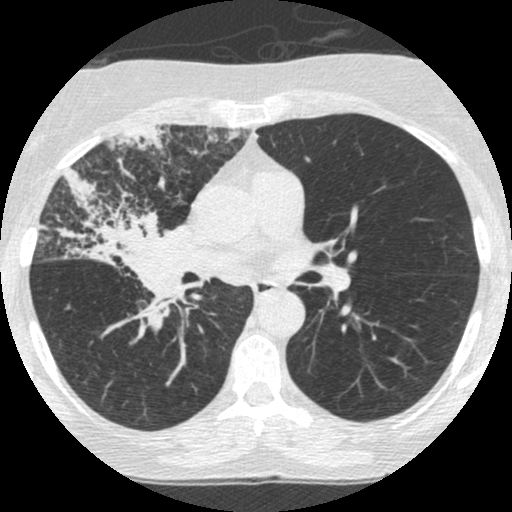
Low-dose screening chest CT, one axial slice; slice 145 of 253 in the series (ordered by position); lung window (W 1500 / L -600 HU); 1.25 mm slice thickness; 512 × 512 image matrix, field of view 294 × 294 mm.
Outlined on this slice (manually delineated by an expert):
- lesion 2 (tumor, hilum of right lung): bounding box (x1, y1, x2, y2) in pixels: (53, 167, 188, 336)
- lesion 3 (tumor, upper lobe of right lung): (104, 124, 171, 155)
- lesion 4 (tumor, upper lobe of right lung): (205, 125, 242, 147)